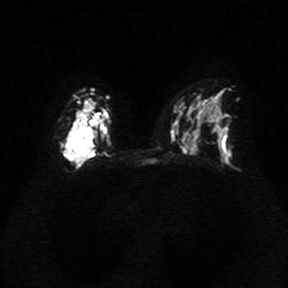
Breast MRI, one axial slice. Slice 19 of 34 in the series (ordered by position). Diffusion-weighted series; image 2 of 4 stored at this slice position (different b-values; order by instance number). 1.5 T. 288 × 288 image matrix, field of view 340 × 340 mm. Female patient.
Outlined on this slice (outlined manually by an expert reader):
- tumour on diffusion-weighted imaging: bounding box (x1, y1, x2, y2) in pixels: (62, 120, 97, 162)